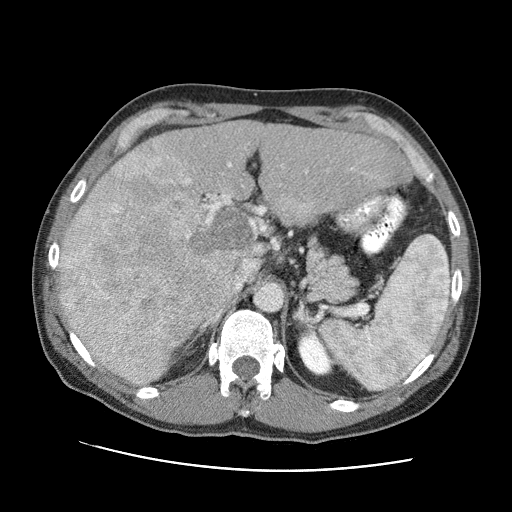
Contrast-enhanced abdominal CT (liver protocol), one axial slice; position 53 of 95 along the scan axis; reconstruction kernel STANDARD; 120 kVp; one of 2 acquisitions stored at this slice position; soft-tissue window (W 400 / L 40 HU); 512 × 512 image matrix, field of view 360 × 360 mm. From the clinical record (not read from this slice): diagnosis: hepatocellular carcinoma (patient treated with transarterial chemoembolisation; whether this scan precedes or follows treatment is not stated here); TNM stage (as recorded): Stage-IVA; Child-Pugh class: A; tumour differentiation: moderately differentiated.
Outlined on this slice (semi-automatic segmentation, software-assisted and operator-edited):
- abdominal aorta: bounding box <256,283,282,310> (left, top, right, bottom; pixels)
- liver parenchyma outside the tumour (the mass and vessels are separate outlines, so this box may not span the whole liver): <58,120,412,384>
- mass: <59,146,254,384>
- liver vessels: <154,145,354,319>